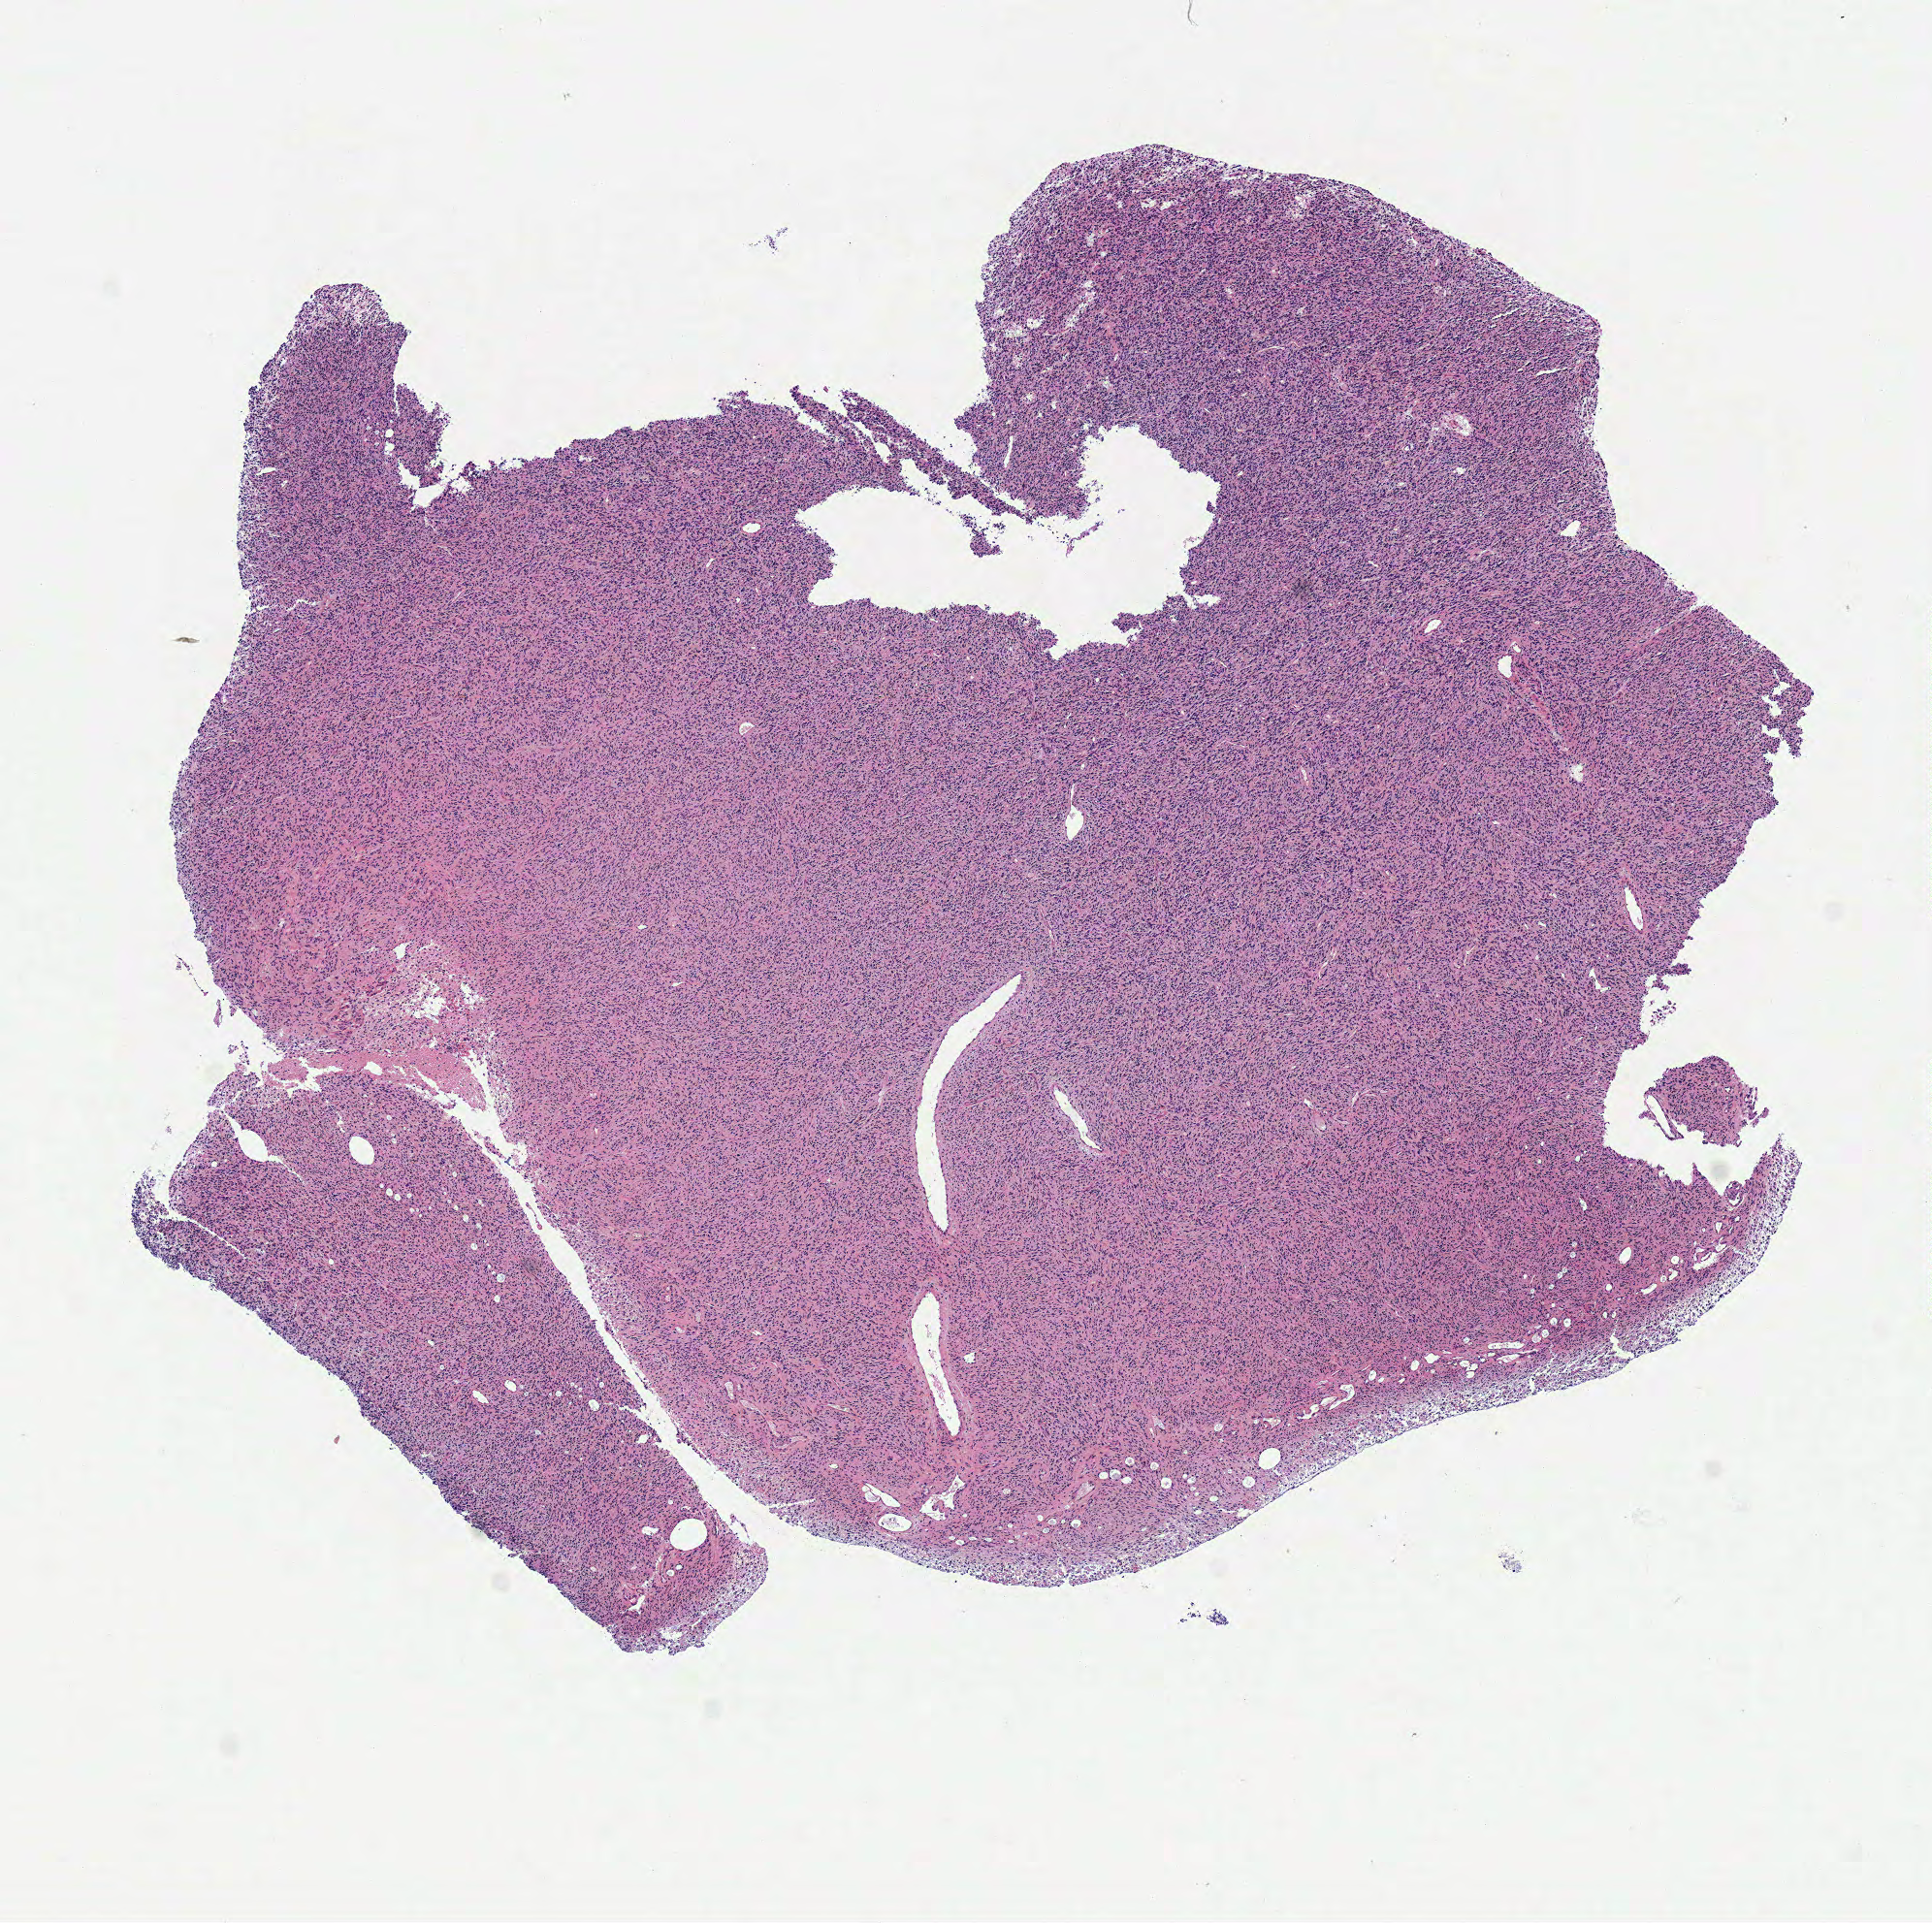
Hematoxylin and eosin (H&E) stained whole-slide image — a low-resolution overview of the entire scanned area, about 7.8 x 7.8 mm; frozen section; primary tumour sample from the brain. Female patient; age at initial diagnosis 59 years. Histologic grade: G3 (poorly differentiated). Pathologist review of this section (percent, as recorded): tumour cells 100%, tumour nuclei 85%, normal cells 0%, stromal cells 0%, necrosis 0%.
Pathologic diagnosis: Mixed glioma (cerebrum).